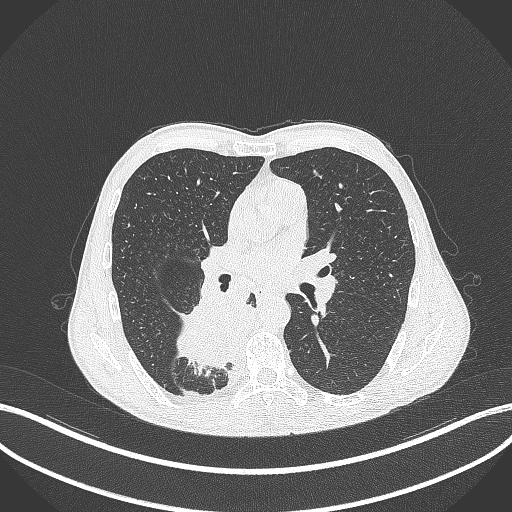
Chest CT, one axial slice; position 203 of 371 along the scan axis; reconstruction kernel B70f; 120 kVp; lung window (W 1500 / L -600 HU); 1 mm slice thickness; 512 × 512 image matrix, field of view 400 × 400 mm. Male patient, age 58 years. From the clinical record (not read from this slice): clinical TNM (as recorded): T3 N1 M1.
Structures marked on this image (bounding box drawn by a radiologist):
- lung tumour (recorded histology: squamous cell carcinoma): box from (x=176, y=293) to (x=249, y=375) px